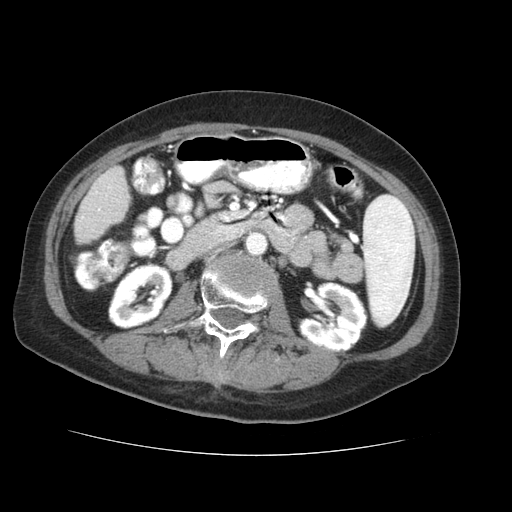
Contrast-enhanced abdominal CT (liver protocol), one axial slice; slice 8 of 73 in the series (ordered by position); 120 kVp; soft-tissue window (W 400 / L 40 HU); 2.5 mm slice thickness; 512 × 512 image matrix, field of view 360 × 360 mm. Case-level facts recorded for this patient, not image findings: diagnosis: hepatocellular carcinoma (patient treated with transarterial chemoembolisation; whether this scan precedes or follows treatment is not stated here); TNM stage (as recorded): Stage-IVB; Child-Pugh class: A; tumour differentiation: well differentiated.
Annotated regions visible in this slice (semi-automatically segmented with operator editing):
- liver parenchyma outside the tumour (the mass and vessels are separate outlines, so this box may not span the whole liver): bounding box [x1, y1, x2, y2] px = [74, 166, 126, 244]
- liver vessels: [81, 195, 107, 219]